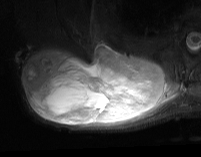
MRI of an extremity soft-tissue mass, one axial slice; slice 37 of 74 in the series (ordered by position); STIR; MR volume resampled by the dataset authors to the PET/CT grid (not the native acquisition matrix); 3.27 mm slice thickness; 201 × 157 image matrix, field of view 196 × 153 mm. Male patient. Case-level facts recorded for this patient, not image findings: histological type: pleiomorphic spindle cell undifferentiated; grade: high; site of the primary tumour: right parascapusular.
Outlined on this slice (expert contour drawn on MRI and transferred to this co-registered scan by the dataset authors):
- gross tumour volume including surrounding oedema: bounding box (x1, y1, x2, y2) in pixels: (23, 43, 182, 127)
- gross tumour volume (mass): (23, 45, 166, 126)